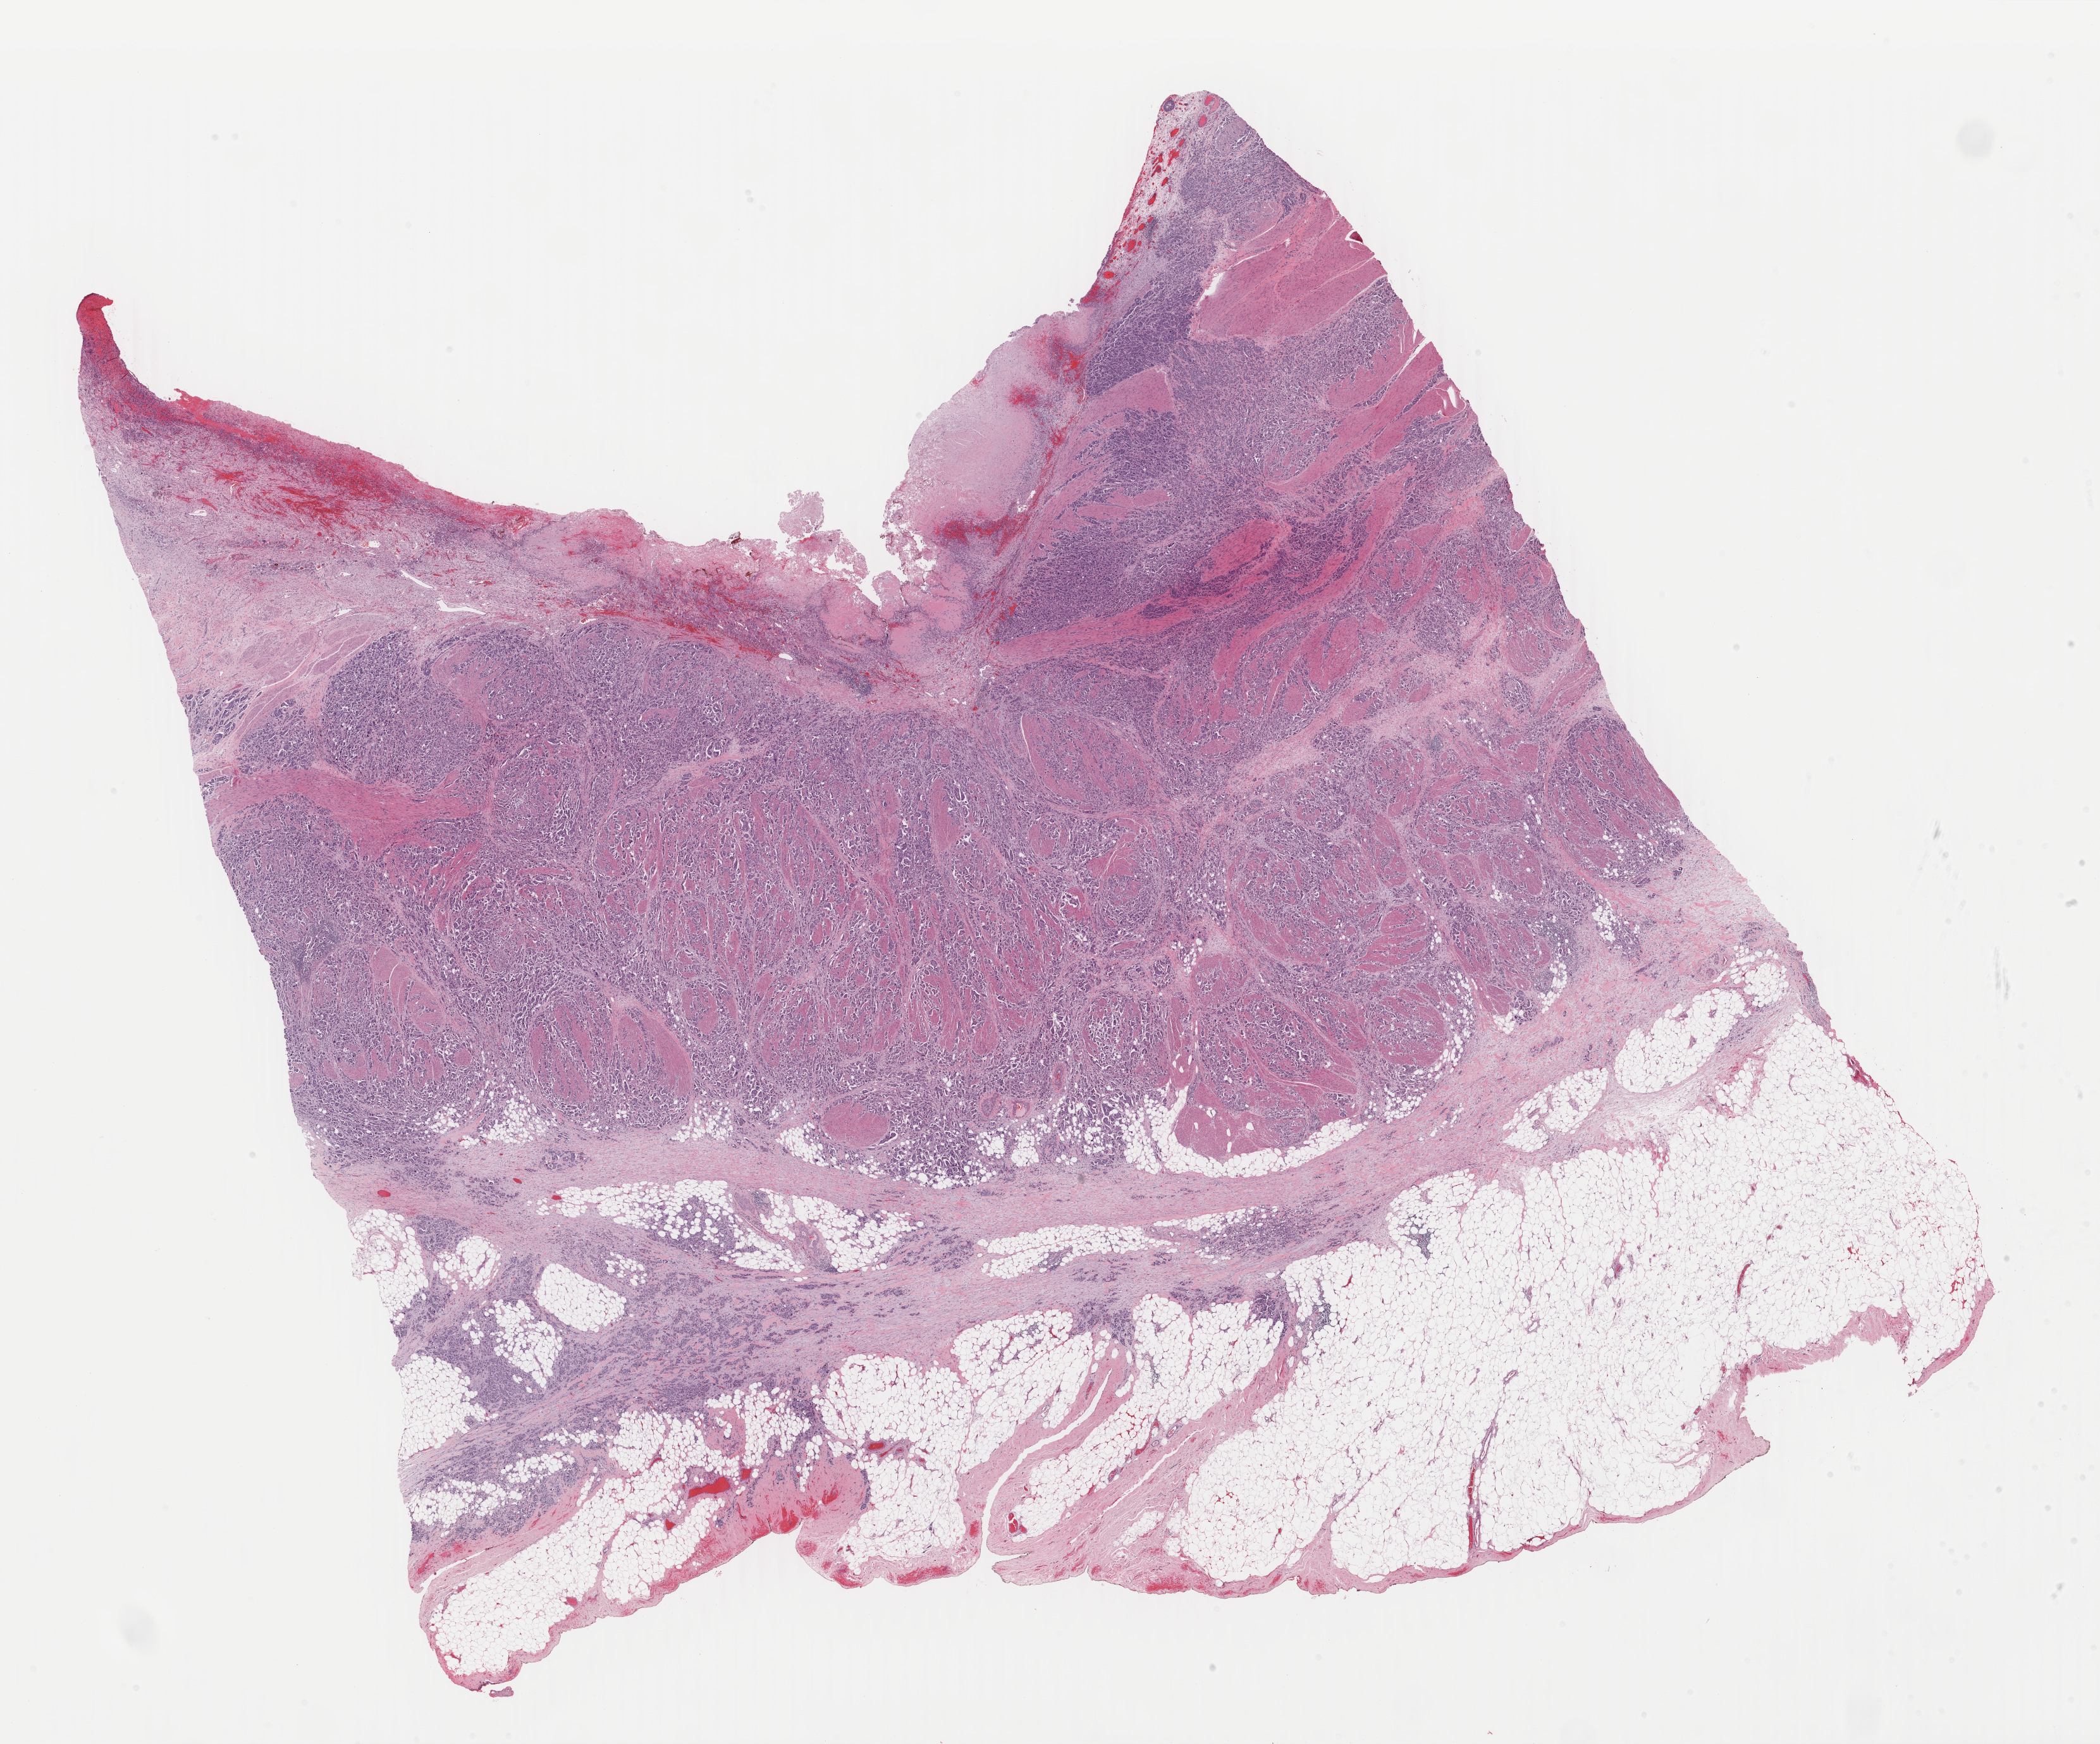
Whole-slide histology image, H&E-stained, shown as a low-resolution overview of the whole scanned area (about 26.4 x 21.9 mm), formalin-fixed paraffin-embedded (FFPE) diagnostic section, sample: primary tumour, bladder. Patient: male, age at initial diagnosis 68 years. Histologic grade: high grade.
• TNM: T4a N2 MX
• lymph nodes positive (case pathology): 4 of 16 examined
• AJCC pathologic stage: IV (7th edition)
• pathologic diagnosis: Transitional cell carcinoma (posterior wall of bladder)